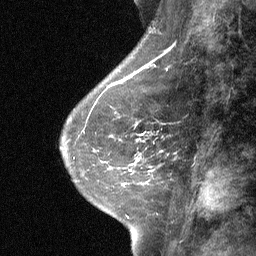
Breast MRI (dynamic contrast-enhanced), one sagittal slice; slice 25 of 64 in the series (ordered by position); dynamic contrast-enhanced study with each time point stored as its own series, time point 2 of 3 at this slice position (early post-contrast, ordered by acquisition time); 1.5 T; TE 4.8 ms, TR 27 ms; 2 mm slice thickness; 256 × 256 image matrix, field of view 180 × 180 mm. Female patient, age 42 years. Case-level facts recorded for this patient, not image findings: setting: breast cancer imaged before/during neoadjuvant chemotherapy; receptor status: triple-negative.
Outlined on this slice (semi-automatic segmentation, software-assisted and operator-edited):
- analysis volume of interest (the breast-tissue region the enhancement analysis was run in; not a lesion): bounding box [x1, y1, x2, y2] px = [99, 117, 174, 187]
- tumour enhancement mask (voxels above the 90 % enhancement threshold inside the analysis volume of interest): [136, 134, 142, 162]